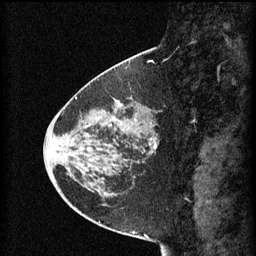
Breast MRI (dynamic contrast-enhanced), one sagittal slice; slice 25 of 60 in the series (ordered by position); 3 images stored at this slice position (order not interpretable as contrast timing); 1.5 T; TE 4.2 ms, TR 8.2 ms; 2 mm slice thickness; 256 × 256 image matrix, field of view 200 × 200 mm. Female patient, age 45 years.
Structures marked on this image (semi-automatic segmentation, software-assisted and operator-edited):
- analysis volume of interest (the breast-tissue region the enhancement analysis was run in; not a lesion): bounding box <80,102,157,171> (left, top, right, bottom; pixels)
- tumour enhancement mask (voxels above the 70 % enhancement threshold inside the analysis volume of interest): <114,118,155,149>